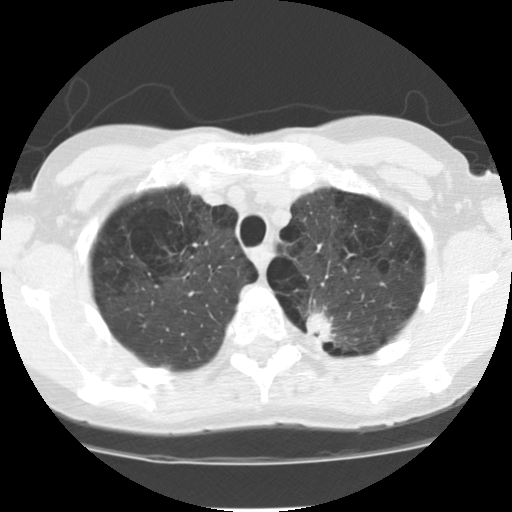
Axial slice from a low-dose chest CT screening exam; baseline annual screen; lung window (W 1500 / L -600 HU); 2.5 mm slice thickness; 120 kVp; slice 22 of 116 in the series. Female, age 61 years at enrolment.
Lesion marked by an expert reader, bounding box <288,302,346,357> (left, top, right, bottom; pixels). The screening reader recorded 4 non-calcified nodules or masses ≥4 mm on this exam (left upper lobe, right lower lobe, right middle lobe, left lower lobe); which of them this box marks is not recorded. Later outcome: lung cancer diagnosed 68 days after this screen — adenocarcinoma, NOS, left upper lobe, poorly differentiated (G3), stage IB (AJCC 6th edition), 17 mm at pathology.